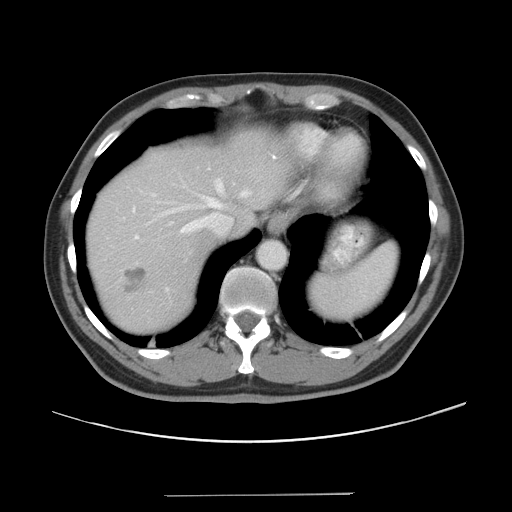
Contrast-enhanced abdominal CT, one axial slice. 120 kVp. Intravenous contrast given. Soft-tissue window (W 400 / L 40 HU). 512 × 512 image matrix, field of view 409 × 409 mm. Male patient, age 65 years. Case-level facts recorded for this patient, not image findings: diagnosis: colorectal cancer liver metastases, imaged before liver resection; multiple liver metastases: no; largest metastasis: 3.8 cm.
Outlined on this slice (expert manual segmentation):
- hepatic veins: bounding box (x1, y1, x2, y2) in pixels: (158, 179, 250, 233)
- liver: (88, 133, 293, 335)
- planned liver remnant (the part of the liver to remain after resection): (88, 133, 293, 306)
- portal vein (with intrahepatic branches): (135, 235, 139, 239)
- liver metastasis: (124, 267, 147, 296)